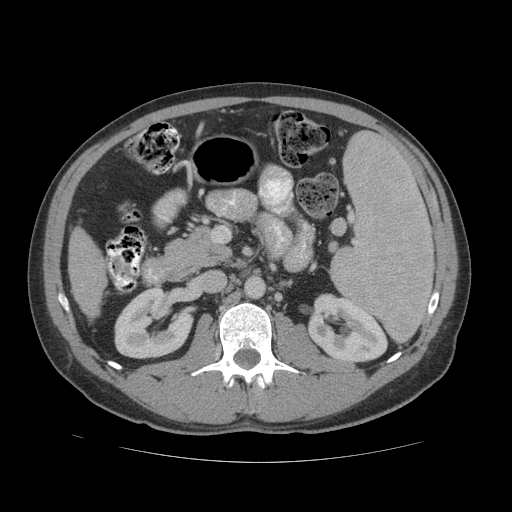
Contrast-enhanced abdominal CT (liver protocol), one axial slice; position 14 of 81 along the scan axis; 140 kVp; soft-tissue window (W 400 / L 40 HU); 2.5 mm slice thickness; 512 × 512 image matrix. From the clinical record (not read from this slice): diagnosis: hepatocellular carcinoma (patient treated with transarterial chemoembolisation; whether this scan precedes or follows treatment is not stated here); TNM stage (as recorded): Stage-IVB; Child-Pugh class: B; tumour differentiation: well differentiated; tumour nodularity: multinodular.
Annotated regions visible in this slice (semi-automatically segmented with operator editing):
- liver parenchyma outside the tumour (the mass and vessels are separate outlines, so this box may not span the whole liver): box from (x=68, y=228) to (x=106, y=316) px